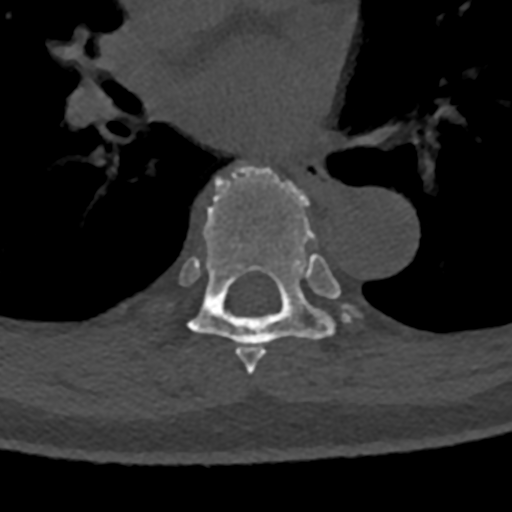
CT including the spine, one axial slice. Position 768 of 797 along the scan axis. Reconstruction kernel Br40s/3. 120 kVp. Bone window (W 1800 / L 400 HU). 0.5 mm slice thickness. 512 × 512 image matrix, field of view 160 × 160 mm. Patient: male, 74 years. From the clinical record (not read from this slice): primary cancer: renal.
Structures marked on this image (semi-automatically segmented with operator editing):
- T6 vertebra: bounding box [x1, y1, x2, y2] px = [238, 346, 265, 375]
- T7 vertebra: [156, 165, 356, 366]